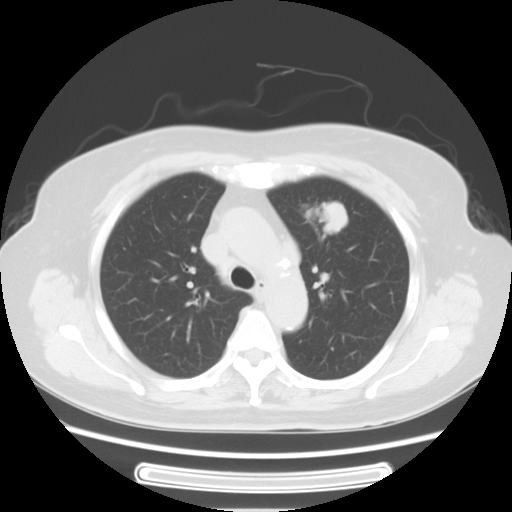
Chest CT, one axial slice. Position 43 of 57 along the scan axis. Lung window (W 1500 / L -600 HU). 5 mm slice thickness. 512 × 512 image matrix. Patient: female, 77 years. Case-level facts recorded for this patient, not image findings: clinical TNM (as recorded): T1c N3 M0.
Structures marked on this image (rectangle marked by the reading radiologist):
- lung tumour (recorded histology: adenocarcinoma): bounding box (x1, y1, x2, y2) in pixels: (296, 194, 357, 235)